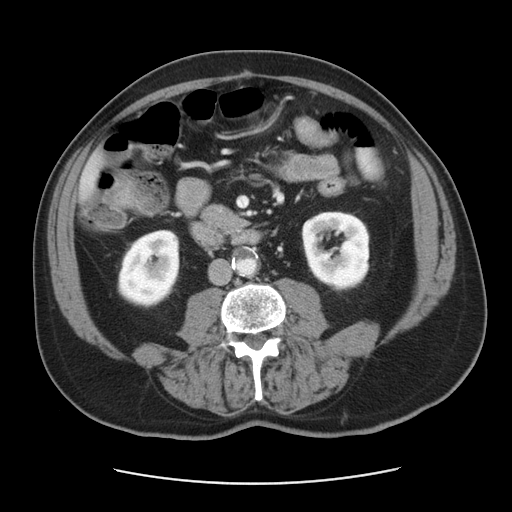
Contrast-enhanced abdominal CT, one axial slice. Position 10 of 42 along the scan axis. Intravenous contrast given. Soft-tissue window (W 400 / L 40 HU). 512 × 512 image matrix, field of view 370 × 370 mm. Male patient, age 73 years. Case-level facts recorded for this patient, not image findings: diagnosis: colorectal cancer liver metastases, imaged before liver resection.
Outlined on this slice (manually delineated by an expert):
- liver: box from (x=84, y=162) to (x=95, y=191) px